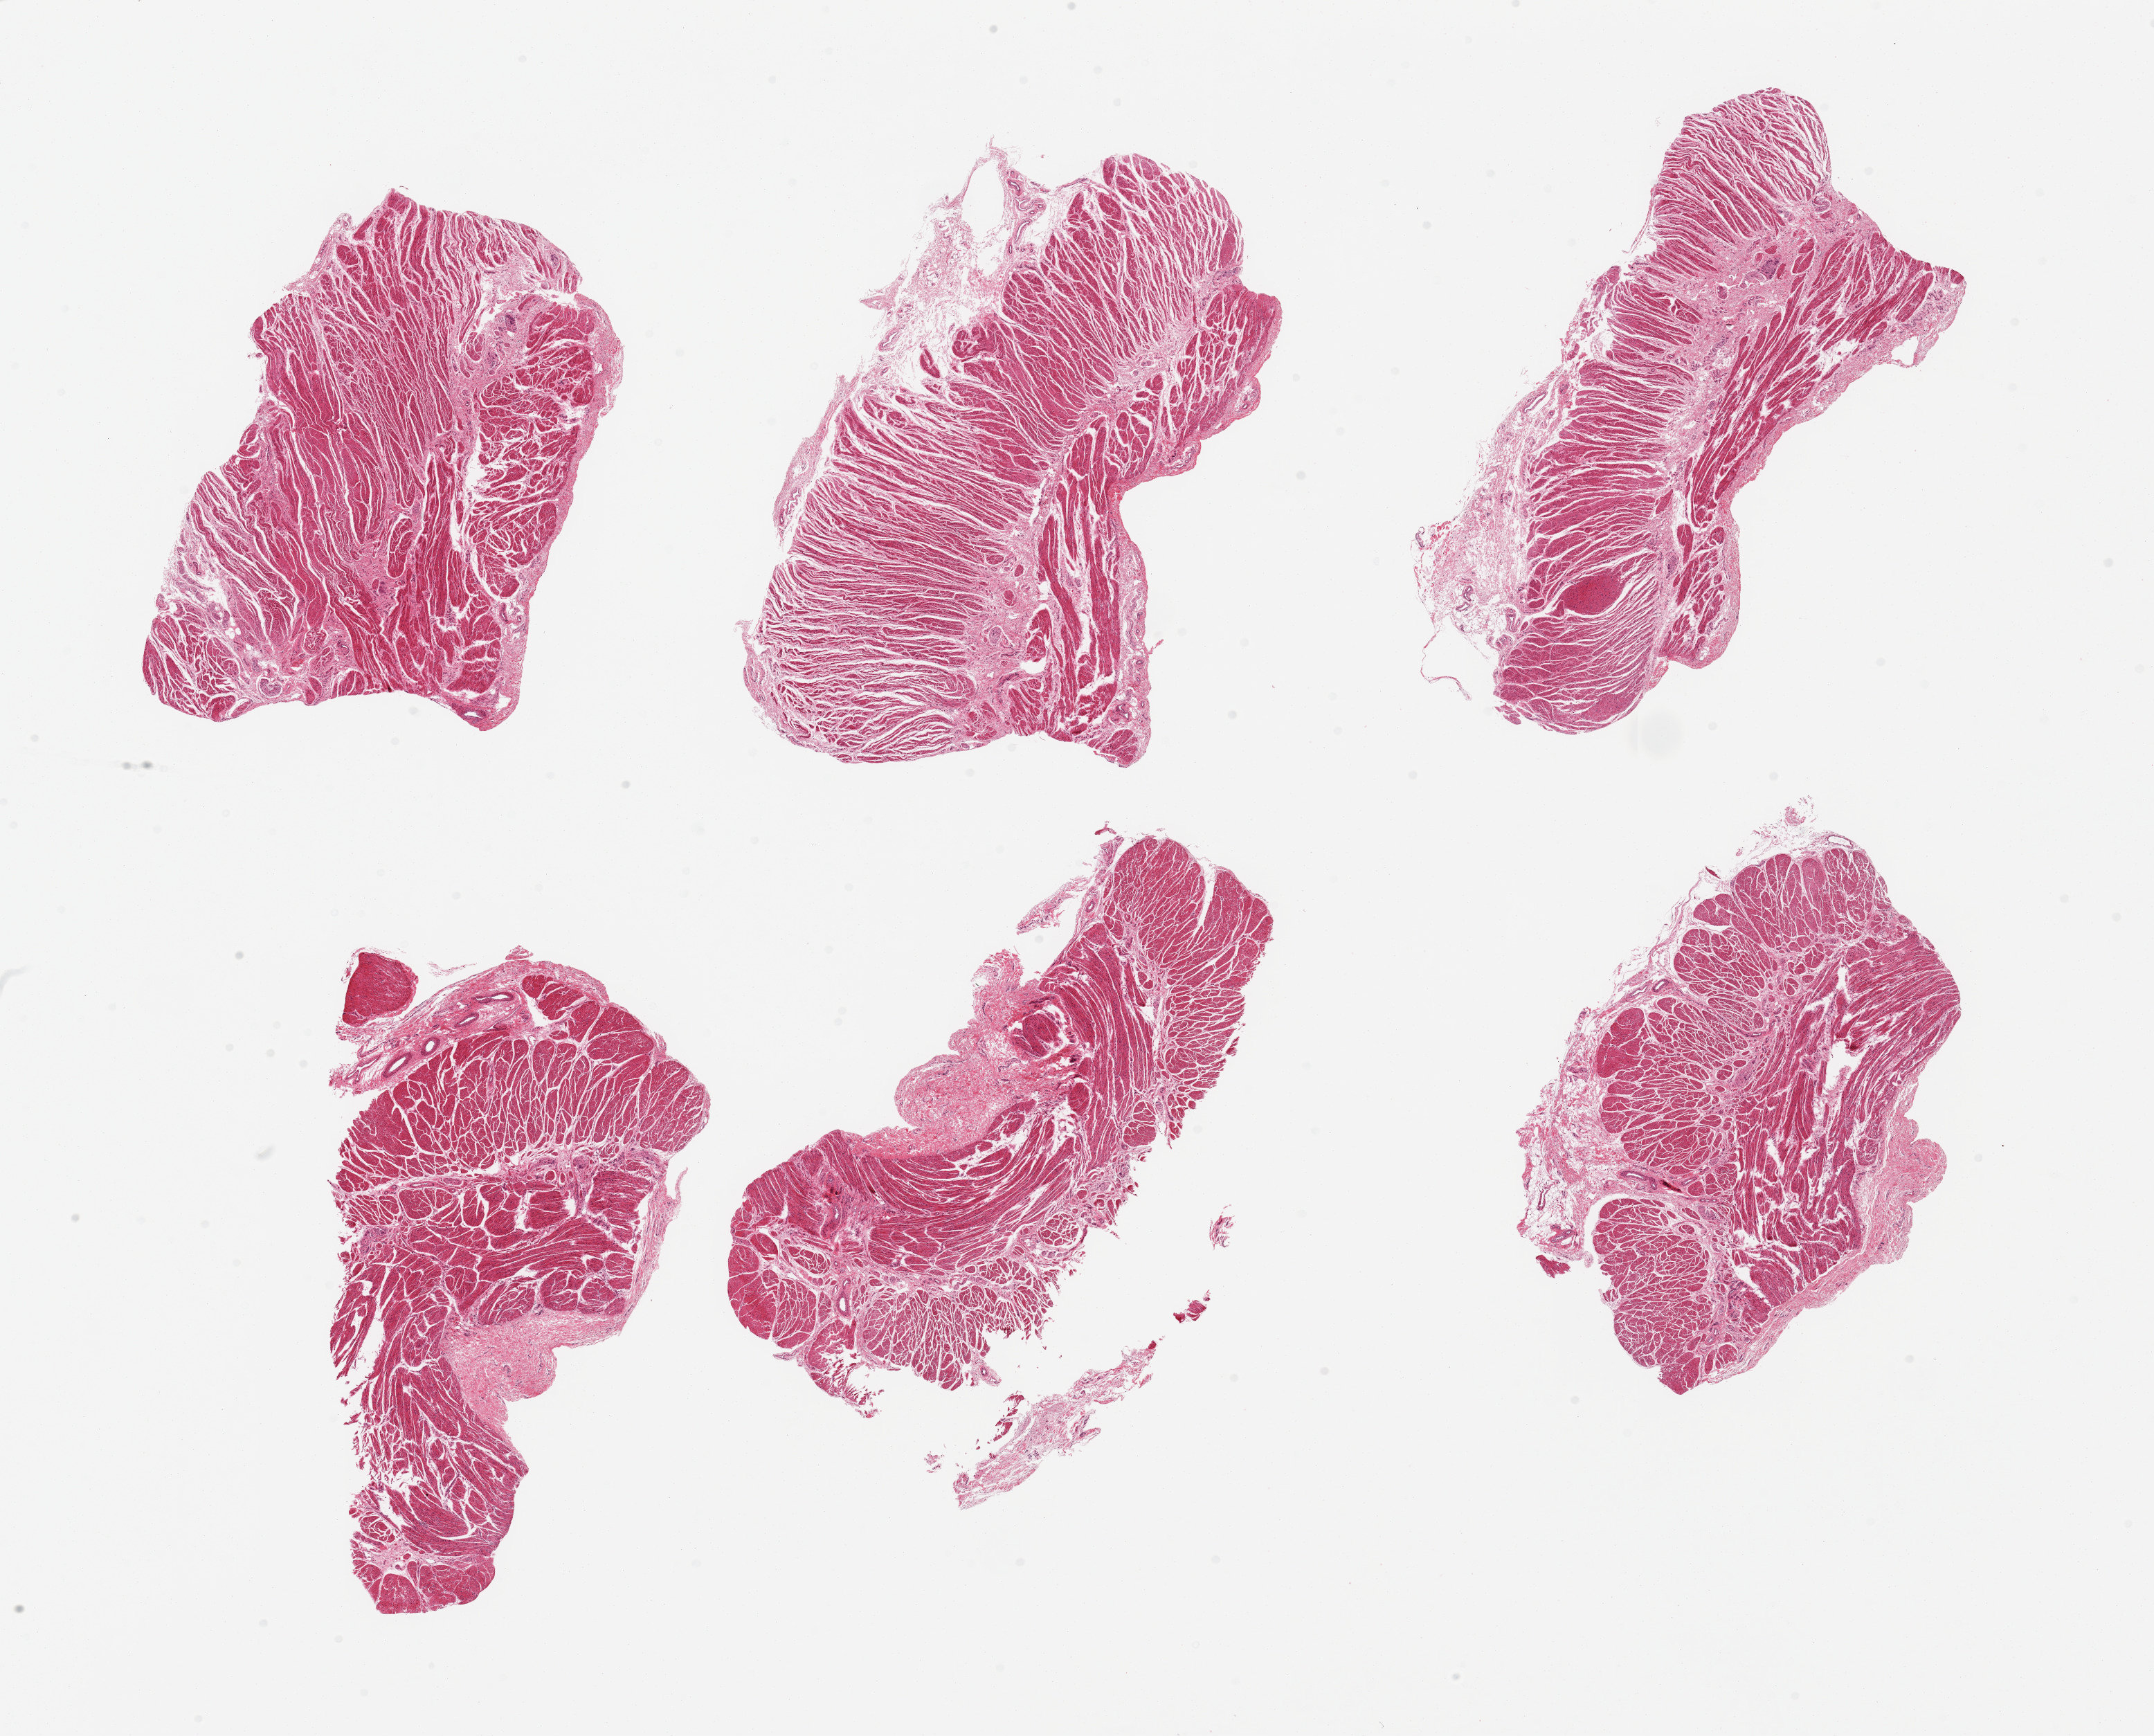
Whole-slide image, hematoxylin and eosin (H&E) stain — a low-resolution overview of the entire scanned area, about 24.6 x 19.8 mm, PAXgene-fixed, paraffin-embedded tissue, target tissue: gastroesophageal junction, donor tissue sample. Donor: female.
Review note (as recorded): 6 pieces, confirmed target muscularis.